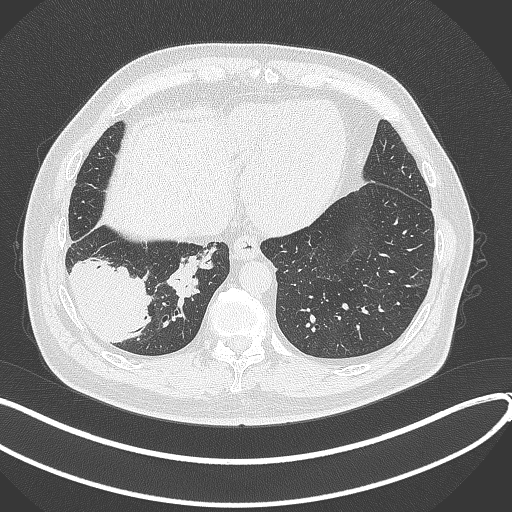
Chest CT, one axial slice; position 83 of 360 along the scan axis; lung window (W 1500 / L -600 HU); 1 mm slice thickness; 512 × 512 image matrix. Male patient, age 59 years.
Structures marked on this image (rectangle marked by the reading radiologist):
- lung tumour (recorded histology: adenocarcinoma): bounding box (x1, y1, x2, y2) in pixels: (71, 251, 154, 345)